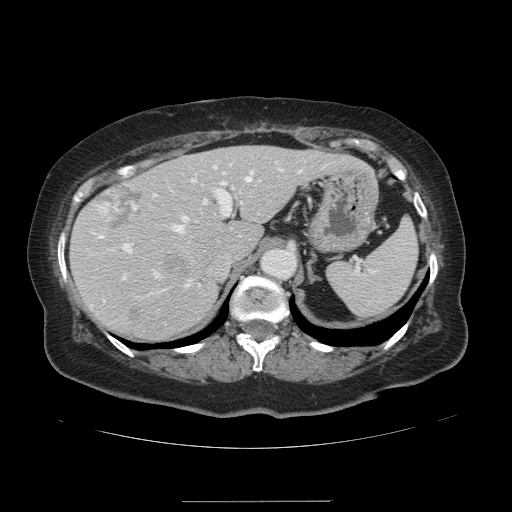
Contrast-enhanced abdominal CT, one axial slice; position 90 of 141 along the scan axis; 120 kVp; intravenous contrast given; soft-tissue window (W 400 / L 40 HU); 512 × 512 image matrix, field of view 393 × 393 mm. Female patient, age 74 years. Case-level facts recorded for this patient, not image findings: diagnosis: colorectal cancer liver metastases, imaged before liver resection; multiple liver metastases: yes; largest metastasis: 7 cm.
Structures marked on this image (manually delineated by an expert):
- hepatic veins: bounding box <99,169,281,298> (left, top, right, bottom; pixels)
- liver: <72,147,355,339>
- planned liver remnant (the part of the liver to remain after resection): <72,147,355,339>
- portal vein (with intrahepatic branches): <123,166,301,278>
- liver metastasis: <99,183,145,234>
- liver metastasis: <165,258,180,270>